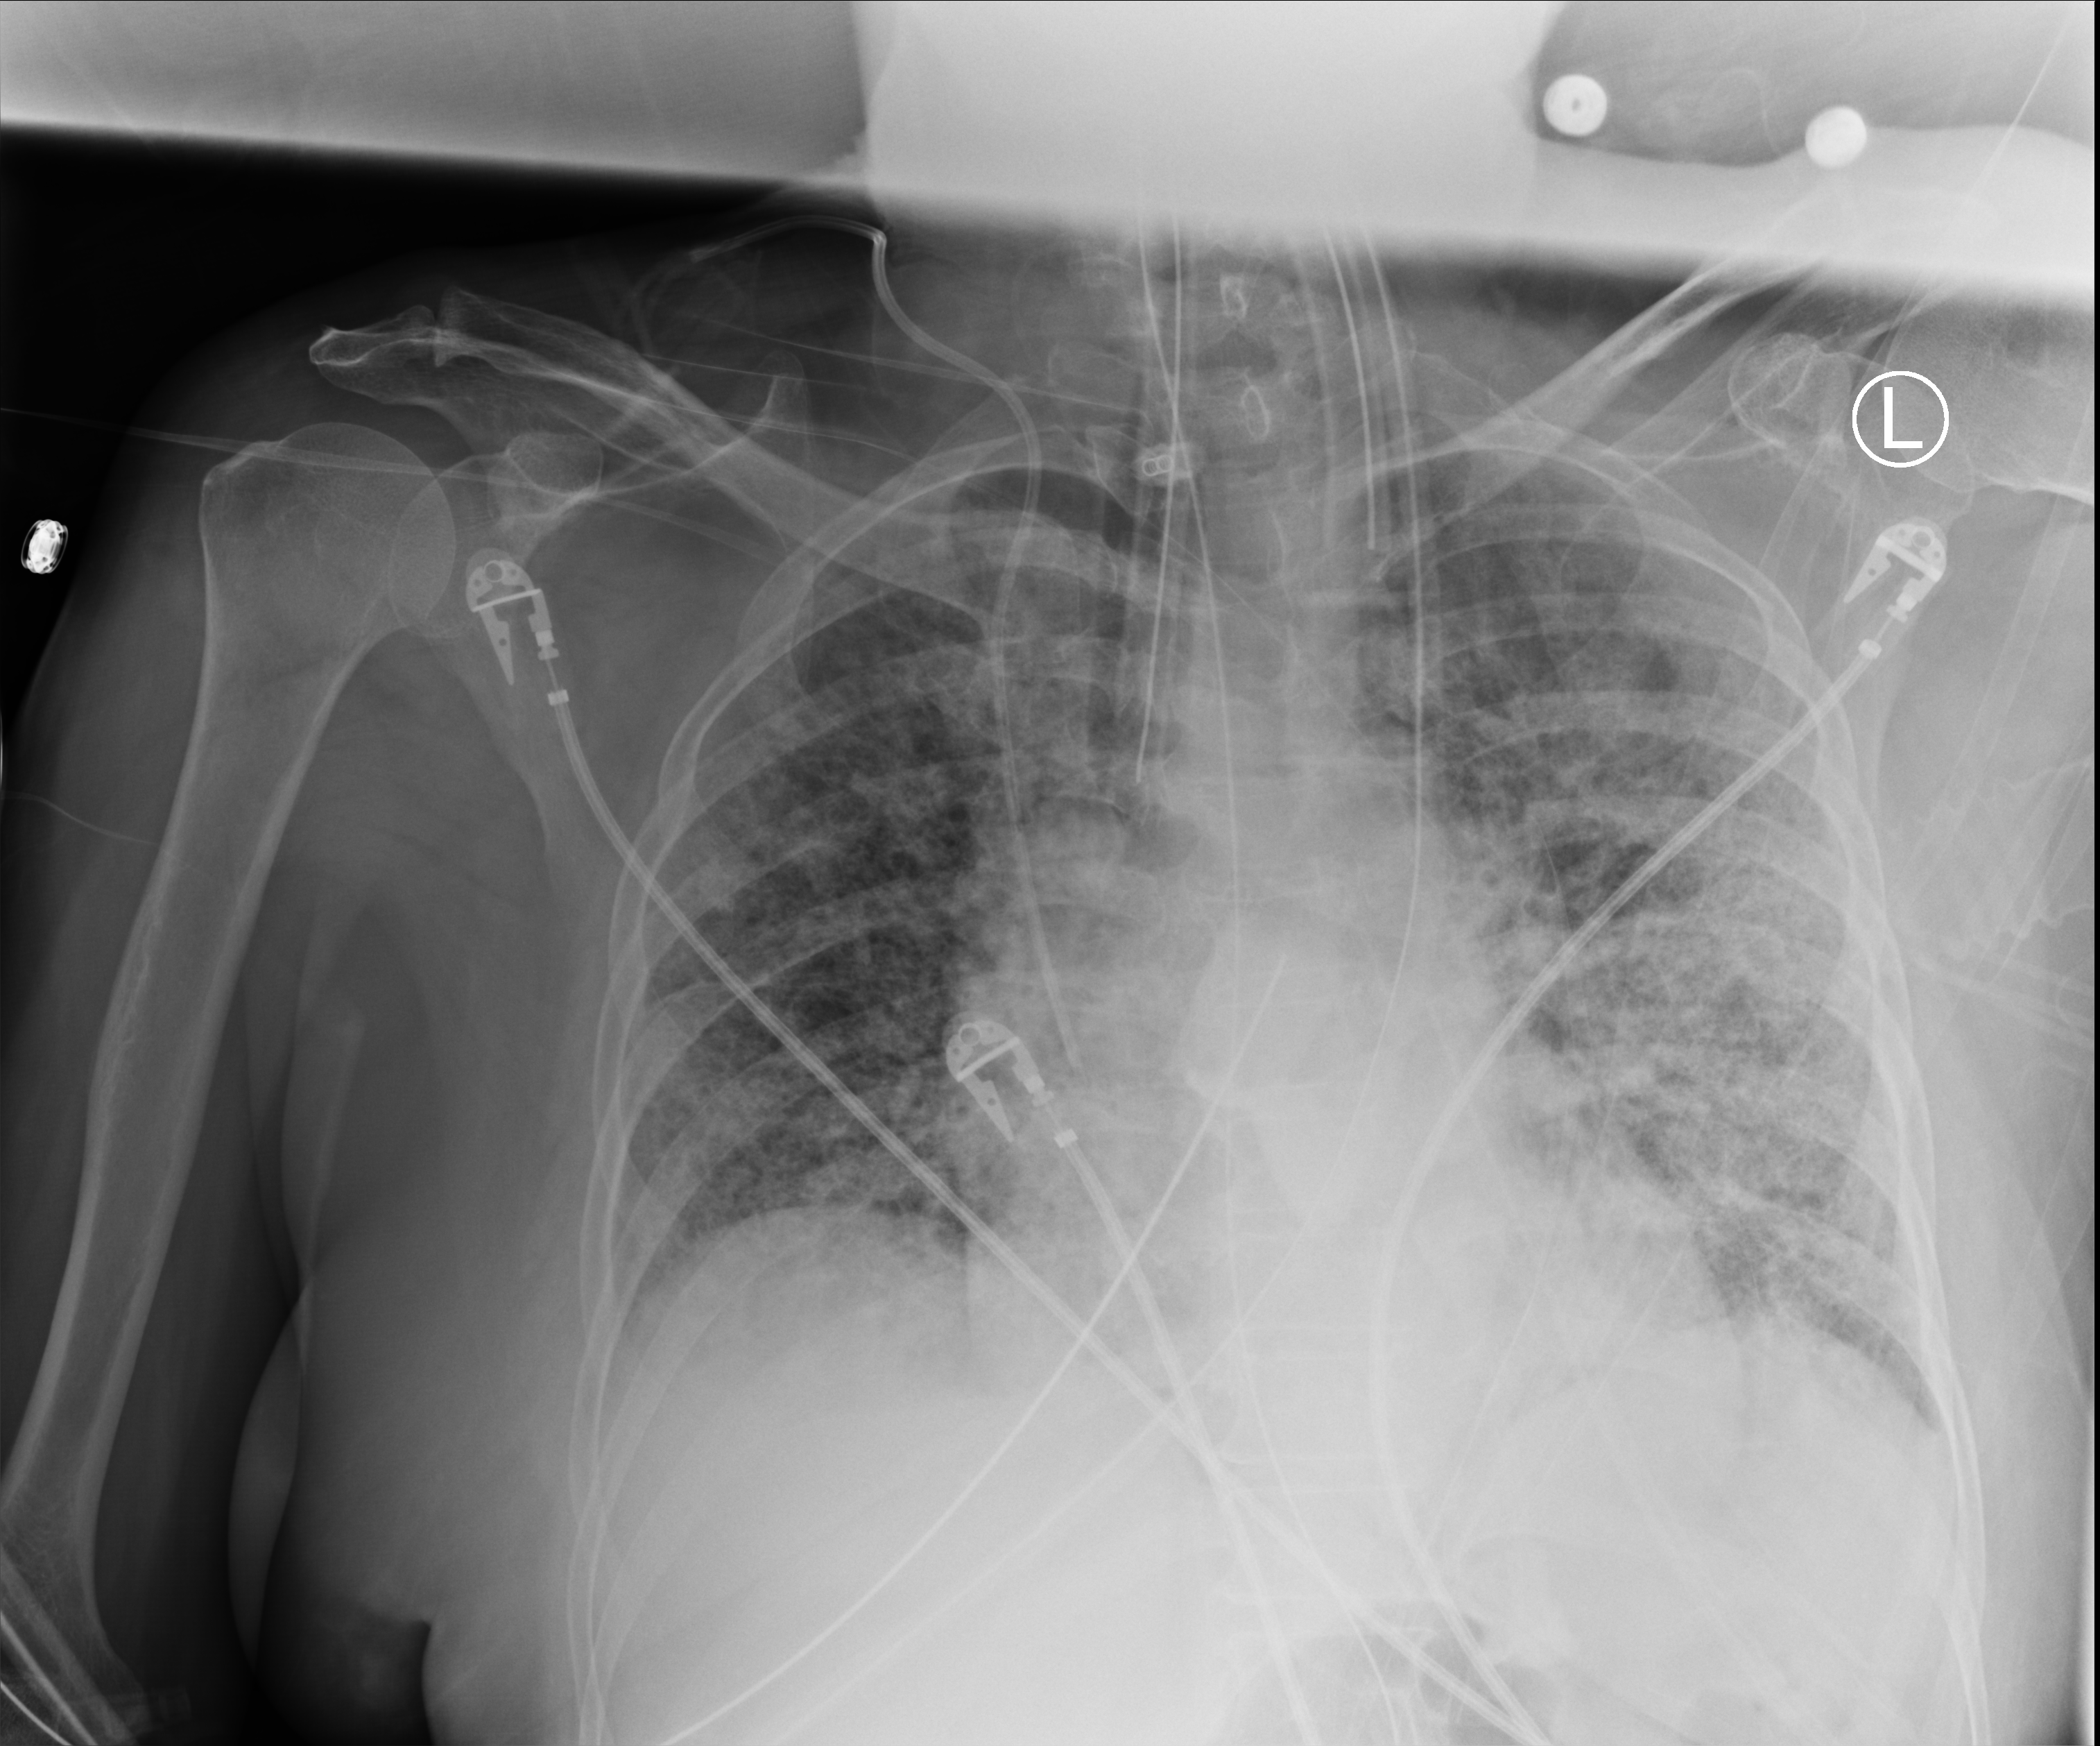
Portable chest radiograph; anteroposterior (AP) projection. Female patient hospitalised with COVID-19, age 60–74 years.
Hospital-stay facts (about this admission, not read from this image; timing relative to this image not recorded): mechanically ventilated during this hospital stay: yes.